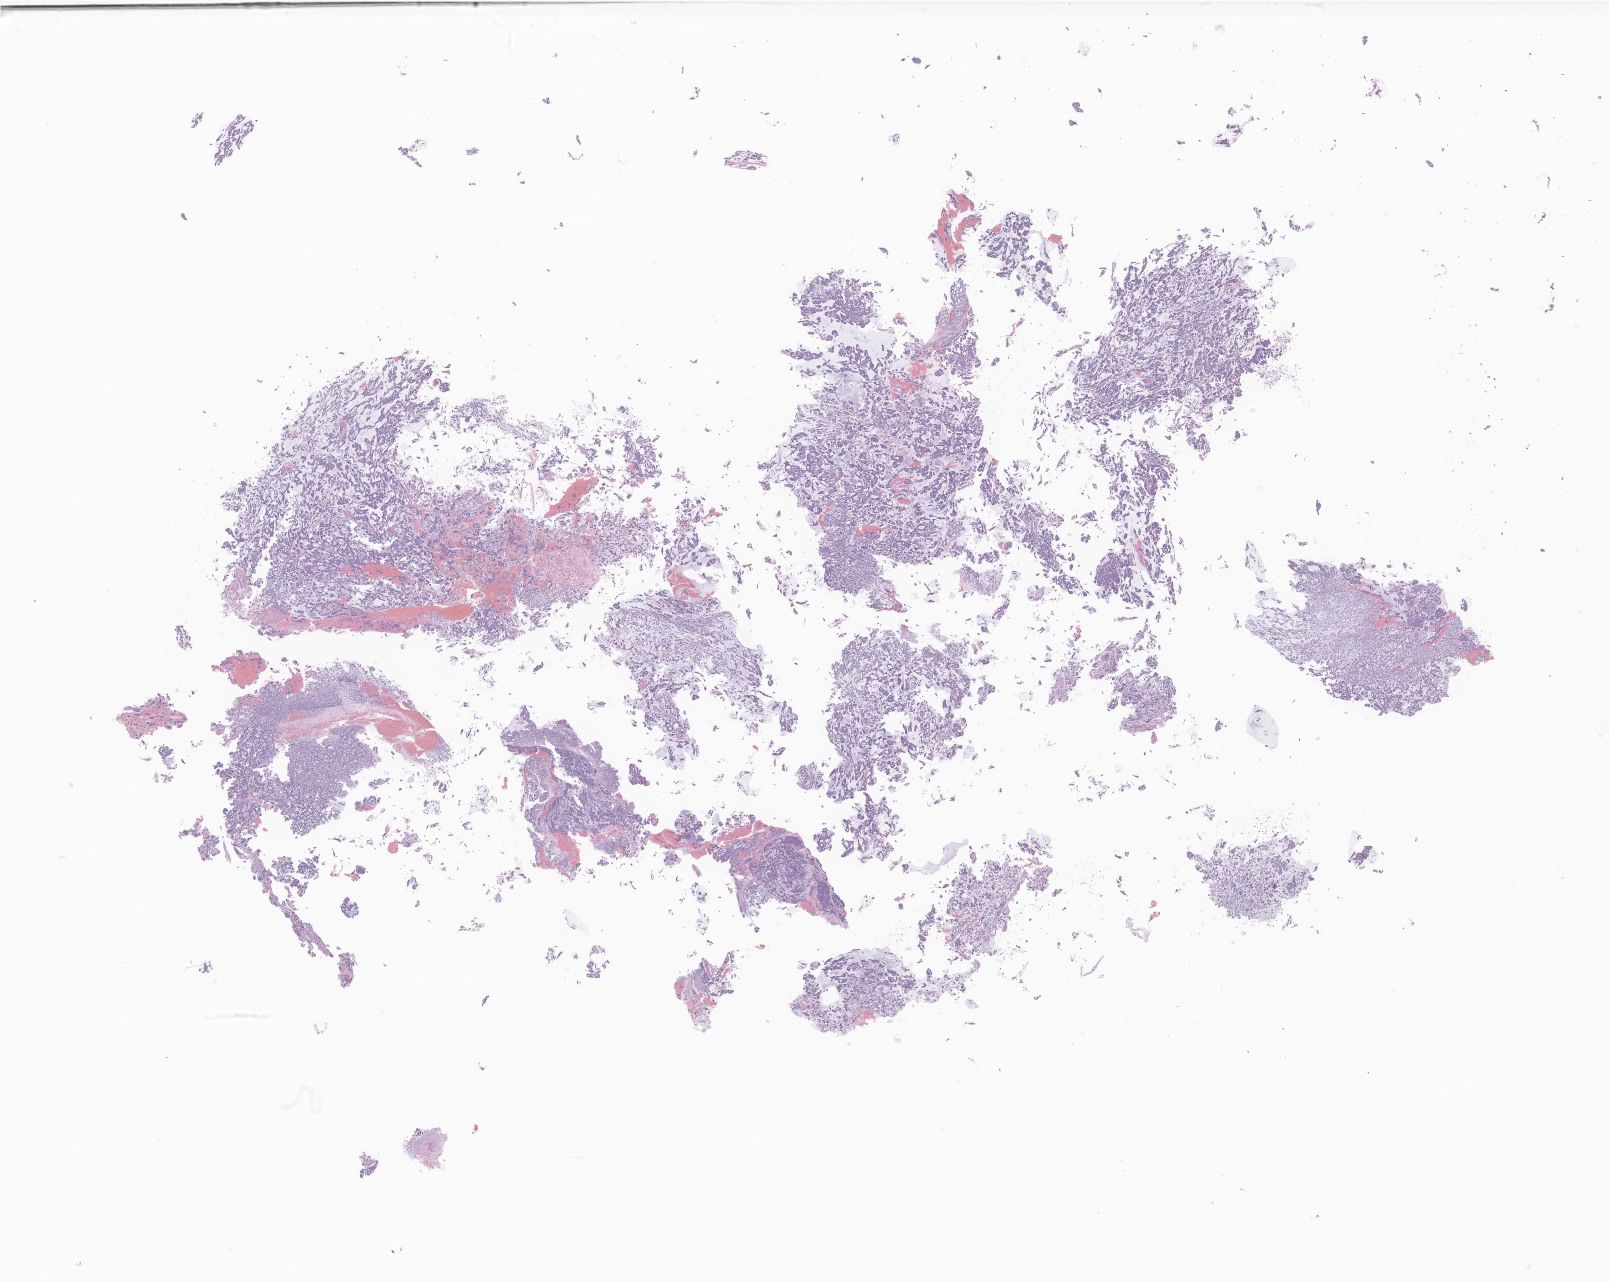
Digitized hematoxylin and eosin (H&E)-stained section of tumor tissue from the brain — whole scanned area (about 27.1 x 21.6 mm) shown as a low-resolution overview. Formalin-fixed, paraffin-embedded (FFPE) tissue. Patient: male, age 50 months (4 years 2 months).
Diagnosis (ICD-O-3 morphology term): Medulloblastoma, NOS.